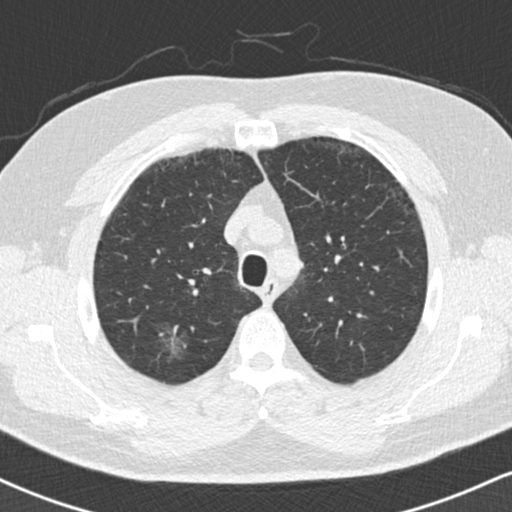
Chest CT (low-dose screening protocol), one axial image; second annual screen; lung window (W 1500 / L -600 HU); 2 mm slice thickness; slice 41 of 169 in the series. Male participant, aged 59 years at enrolment. Current smoker at enrolment.
- Expert reader's lesion annotation, bounding box (x1, y1, x2, y2) in pixels: (152, 310, 204, 364).
- Reader record for this screening exam (exam-level; its link to the box is not recorded): non-calcified nodule or mass ≥4 mm, right upper lobe, 18 × 16 mm, ground glass attenuation, pre-existing on the prior screen: yes.
- Official screen result: positive, no significant change: stable abnormalities potentially related to lung cancer, unchanged since the prior screening exam.
- Participant outcome: lung cancer diagnosed 60 days after this screen — bronchiolo-alveolar adenocarcinoma, NOS, right lower lobe, stage IA (AJCC 6th edition), 15 mm at pathology.